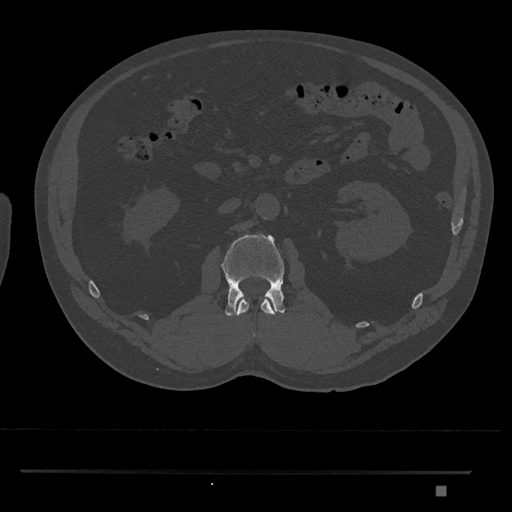
CT including the spine, one axial slice; position 776 of 1134 along the scan axis; reconstruction kernel Br40s/3; 120 kVp; bone window (W 1800 / L 400 HU); 0.5 mm slice thickness; 512 × 512 image matrix, field of view 429 × 429 mm. Male patient, age 65 years. Case-level facts recorded for this patient, not image findings: primary cancer: prostate.
Outlined on this slice (semi-automatic segmentation, software-assisted and operator-edited):
- L1 vertebra: bounding box (x1, y1, x2, y2) in pixels: (236, 298, 275, 337)
- L2 vertebra: (221, 234, 285, 316)